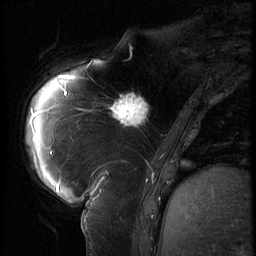
Breast MRI (dynamic contrast-enhanced), one sagittal slice. Slice 19 of 62 in the series (ordered by position). 3 images stored at this slice position (order not interpretable as contrast timing). 1.5 T. TE 4.2 ms, TR 9 ms. 2.5 mm slice thickness. 256 × 256 image matrix. Patient: female, 57 years. From the clinical record (not read from this slice): setting: breast cancer imaged before/during neoadjuvant chemotherapy; receptor status: triple-negative.
Outlined on this slice (semi-automatic segmentation, software-assisted and operator-edited):
- analysis volume of interest (the breast-tissue region the enhancement analysis was run in; not a lesion): bounding box (x1, y1, x2, y2) in pixels: (105, 84, 158, 135)
- tumour enhancement mask (voxels above the 140 % enhancement threshold inside the analysis volume of interest): (110, 92, 150, 127)